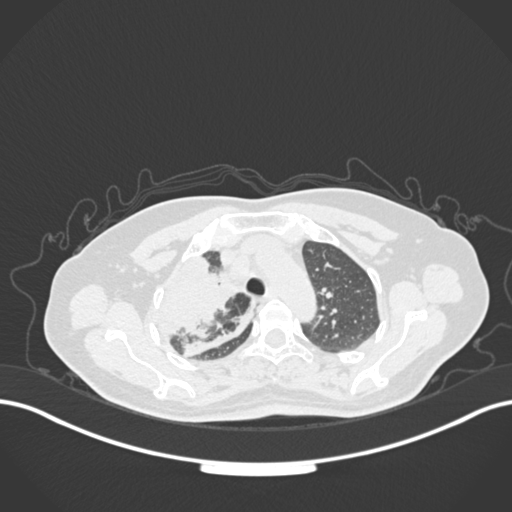
Chest CT, one axial slice; slice 124 of 177 in the series (ordered by position); 120 kVp; lung window (W 1500 / L -600 HU); 1 mm slice thickness; 512 × 512 image matrix, field of view 400 × 400 mm. Female patient, age 60 years. Case-level facts recorded for this patient, not image findings: clinical TNM (as recorded): T3 N1 M1.
Structures marked on this image (rectangle marked by the reading radiologist):
- lung tumour (recorded histology: adenocarcinoma): bounding box (x1, y1, x2, y2) in pixels: (141, 252, 244, 354)